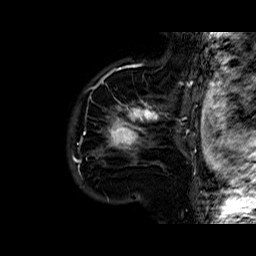
Breast MRI (dynamic contrast-enhanced), one sagittal slice. Slice 47 of 60 in the series (ordered by position). Dynamic contrast-enhanced series, time point 2 of 6 at this slice position (early post-contrast). 1.5 T. TE 6.4 ms, TR 32.8 ms. 4 mm slice thickness. 256 × 256 image matrix, field of view 200 × 200 mm. Female patient. Case-level facts recorded for this patient, not image findings: setting: breast cancer imaged before/during neoadjuvant chemotherapy; receptor status: HR-positive, HER2-negative.
Annotated regions visible in this slice (semi-automatic segmentation, software-assisted and operator-edited):
- analysis volume of interest (the breast-tissue region the enhancement analysis was run in; not a lesion): bounding box (x1, y1, x2, y2) in pixels: (86, 77, 163, 168)
- tumour enhancement mask (voxels above the 100 % enhancement threshold inside the analysis volume of interest): (106, 101, 159, 152)